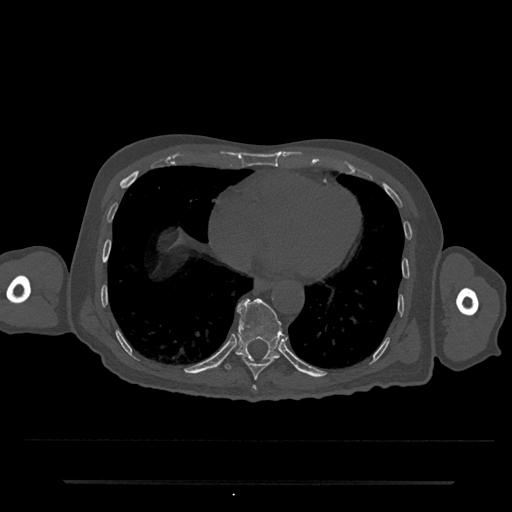
CT including the spine, one axial slice; slice 339 of 797 in the series (ordered by position); 120 kVp; bone window (W 1800 / L 400 HU); 512 × 512 image matrix, field of view 427 × 427 mm. Male patient, age 74 years. From the clinical record (not read from this slice): primary cancer: prostate.
Structures marked on this image (semi-automatically segmented with operator editing):
- T10 vertebra: bounding box (x1, y1, x2, y2) in pixels: (225, 298, 285, 370)
- T8 vertebra: (252, 385, 257, 391)
- T9 vertebra: (241, 356, 276, 380)